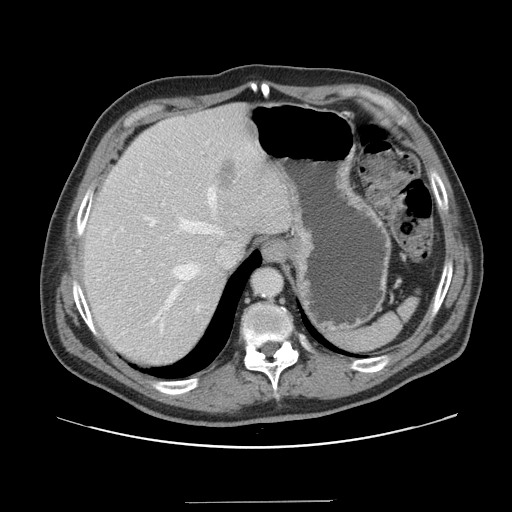
Contrast-enhanced abdominal CT, one axial slice. Slice 122 of 151 in the series (ordered by position). Soft-tissue window (W 400 / L 40 HU). 512 × 512 image matrix. Male patient, age 63 years. Case-level facts recorded for this patient, not image findings: diagnosis: colorectal cancer liver metastases, imaged before liver resection; multiple liver metastases: no; largest metastasis: 2.1 cm; disease in both lobes: no.
Annotated regions visible in this slice (outlined manually by an expert reader):
- hepatic veins: box from (x=144, y=186) to (x=223, y=330) px
- liver: (x=83, y=105)–(x=292, y=367)
- planned liver remnant (the part of the liver to remain after resection): (x=83, y=117)–(x=254, y=366)
- portal vein (with intrahepatic branches): (x=136, y=203)–(x=164, y=282)
- liver metastasis: (x=217, y=159)–(x=238, y=191)